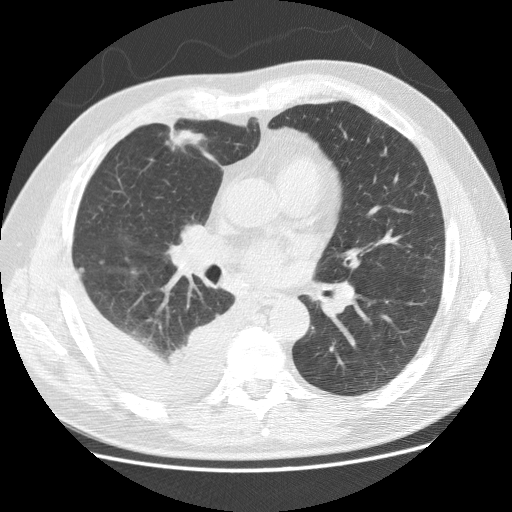
Low-dose screening chest CT, one axial slice. Slice 67 of 142 in the series (ordered by position). 120 kVp. Lung window (W 1500 / L -600 HU). 512 × 512 image matrix.
Annotated regions visible in this slice (outlined manually by an expert reader):
- lesion 1 (tumor, middle lobe of right lung): bounding box (x1, y1, x2, y2) in pixels: (167, 129, 205, 150)